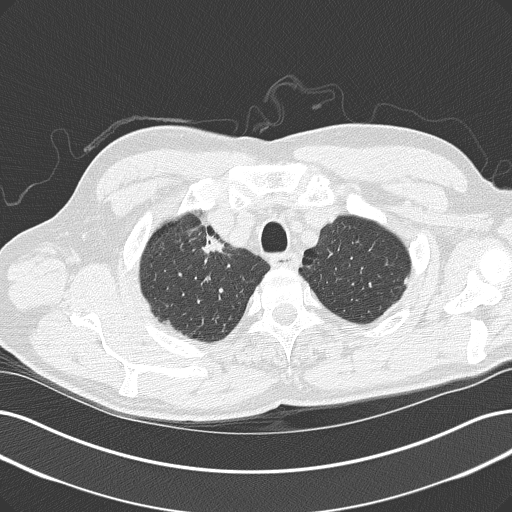
Chest CT (low-dose screening protocol), one axial image. Baseline screening round. Lung window (W 1500 / L -600 HU). 120 kVp. 512 × 512 image matrix. Male participant, aged 61 years at enrolment.
- Expert reader's lesion annotation, bounding box (x1, y1, x2, y2) in pixels: (192, 226, 246, 271).
- The screening reader recorded 2 non-calcified nodules or masses ≥4 mm on this exam; which of them this box marks is not recorded.
- Official screen result: positive, change unspecified: nodule(s) >= 4 mm or enlarging nodule(s), mass(es), or other non-specific abnormalities suspicious for lung cancer.